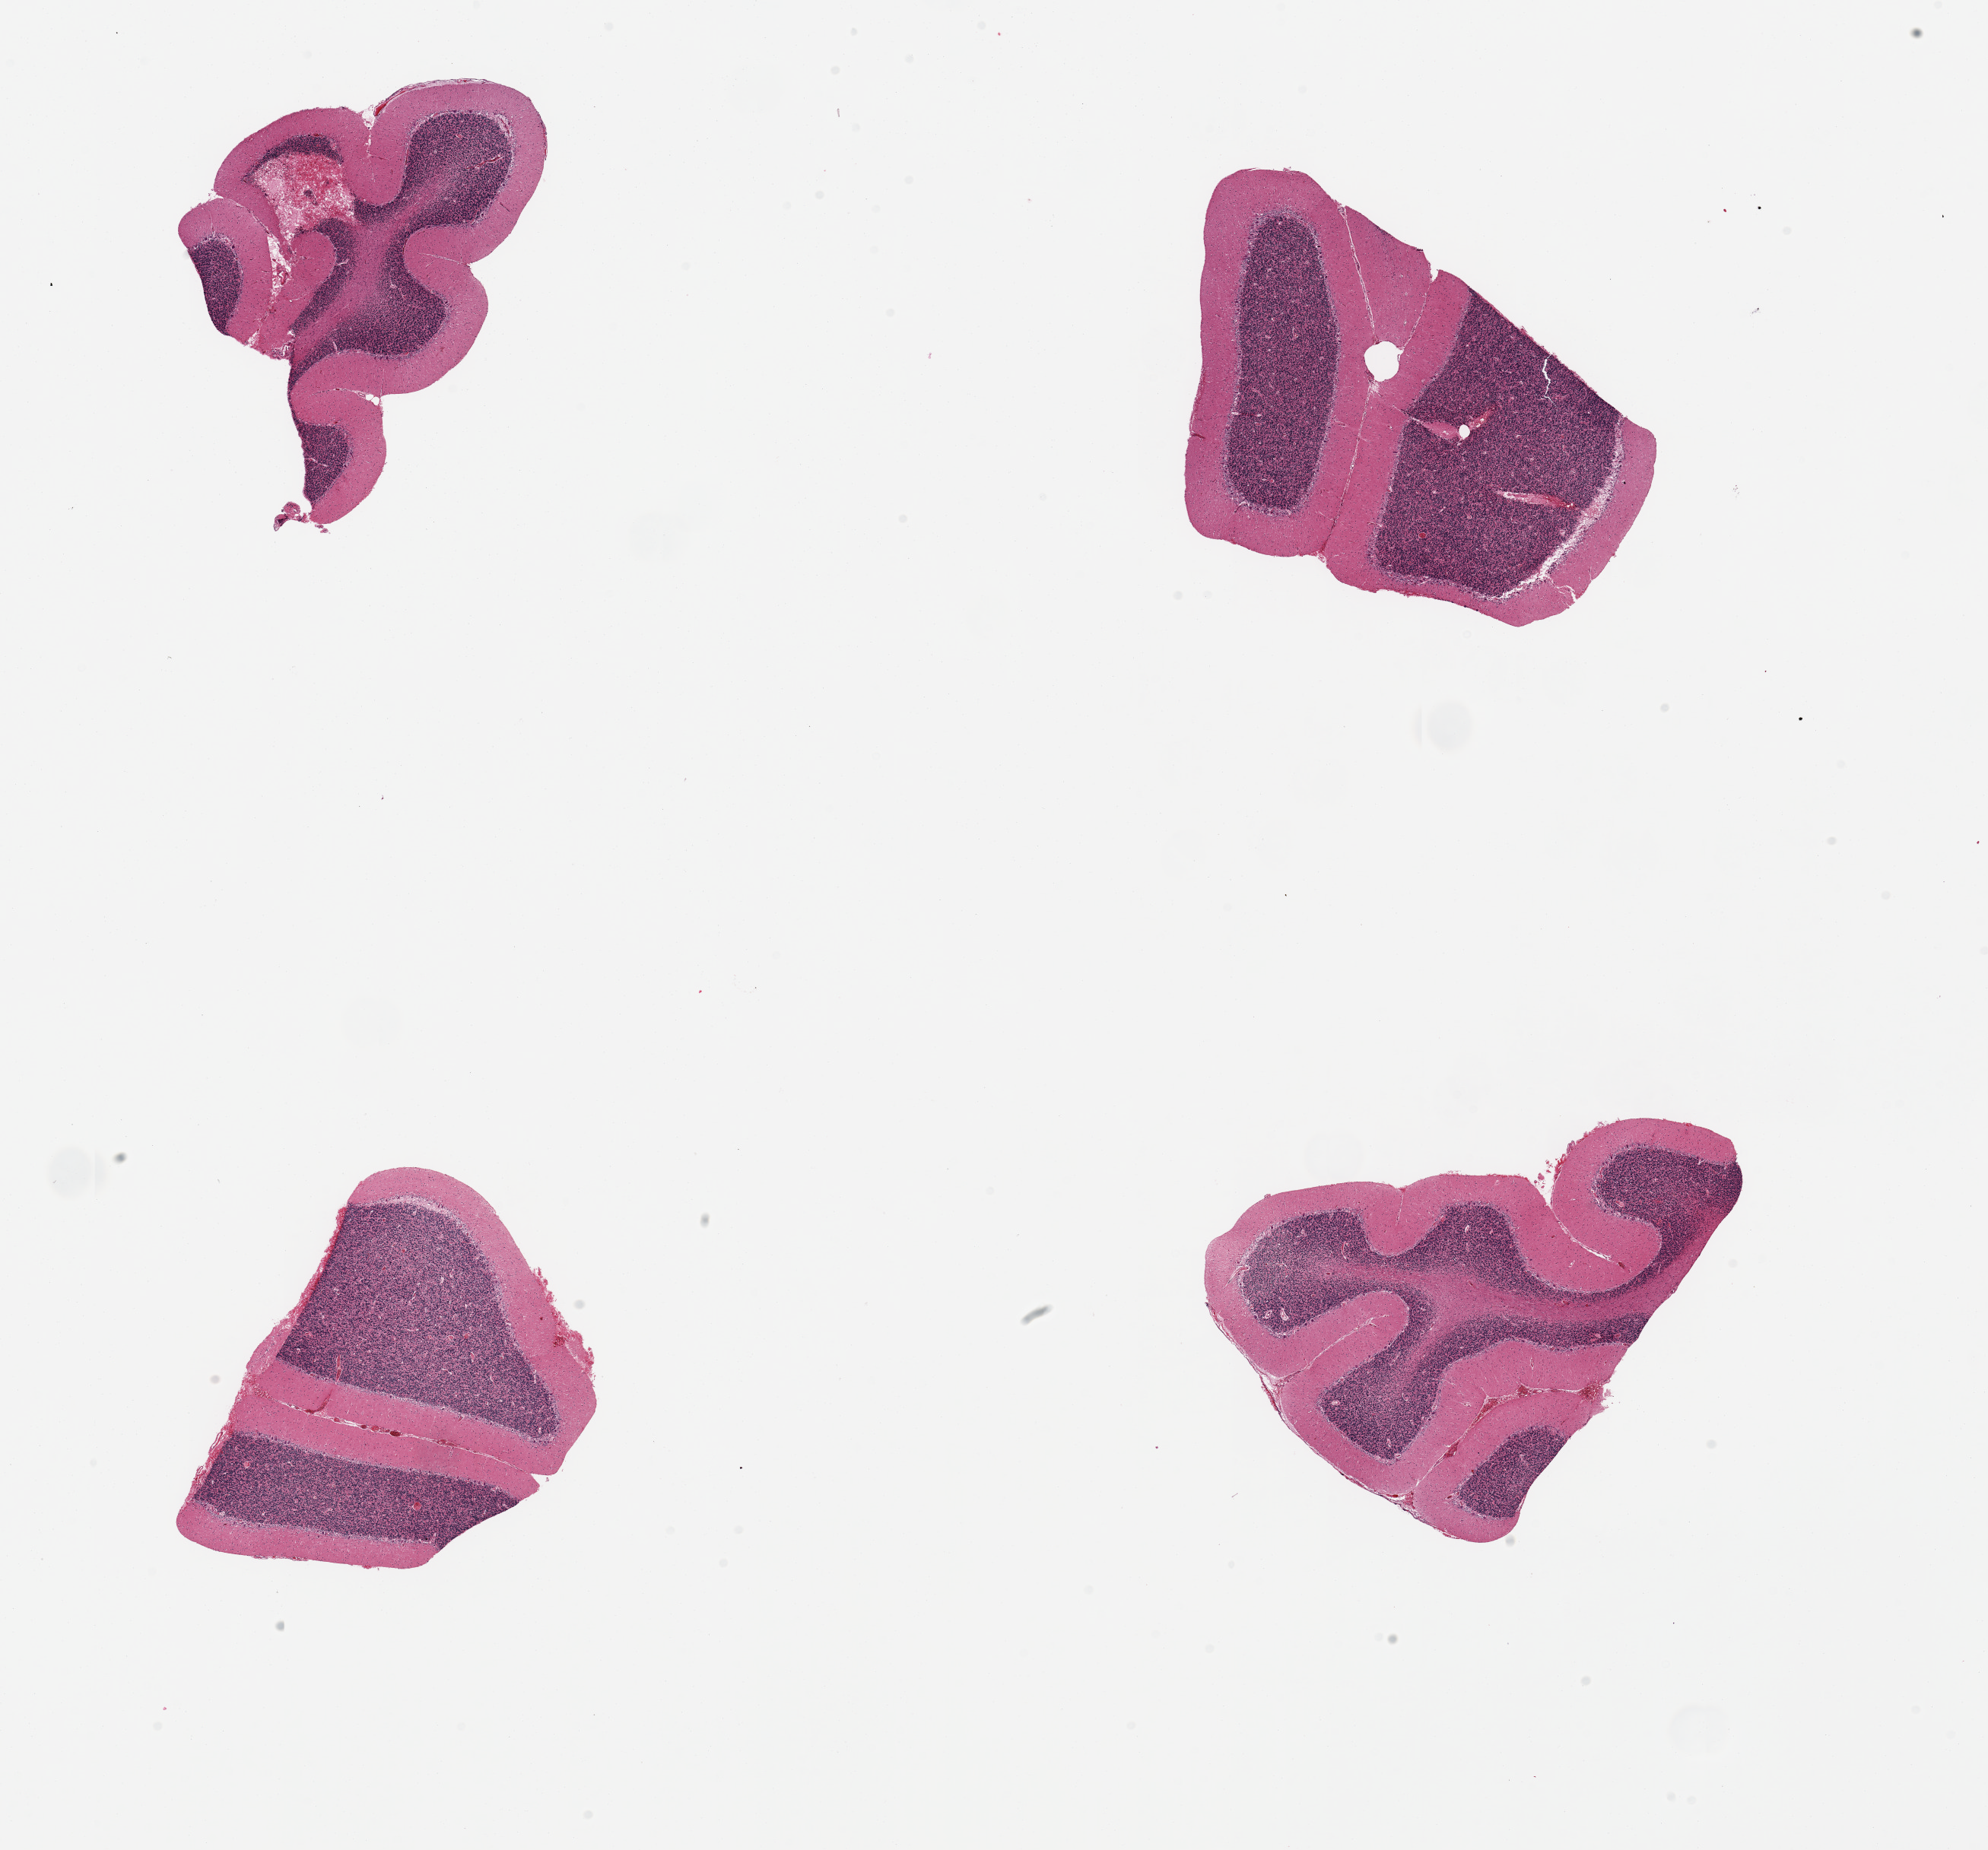
Haematoxylin and eosin whole-slide image — low-resolution overview of the scanned area, about 20.7 x 19.2 mm (acquisition: 20x scan); PAXgene-fixed paraffin-embedded (PFPE) section; target tissue: cerebellum; tissue donor sample. Donor: male.
* review note (as recorded): 4 pieces; mild to moderate autolysis